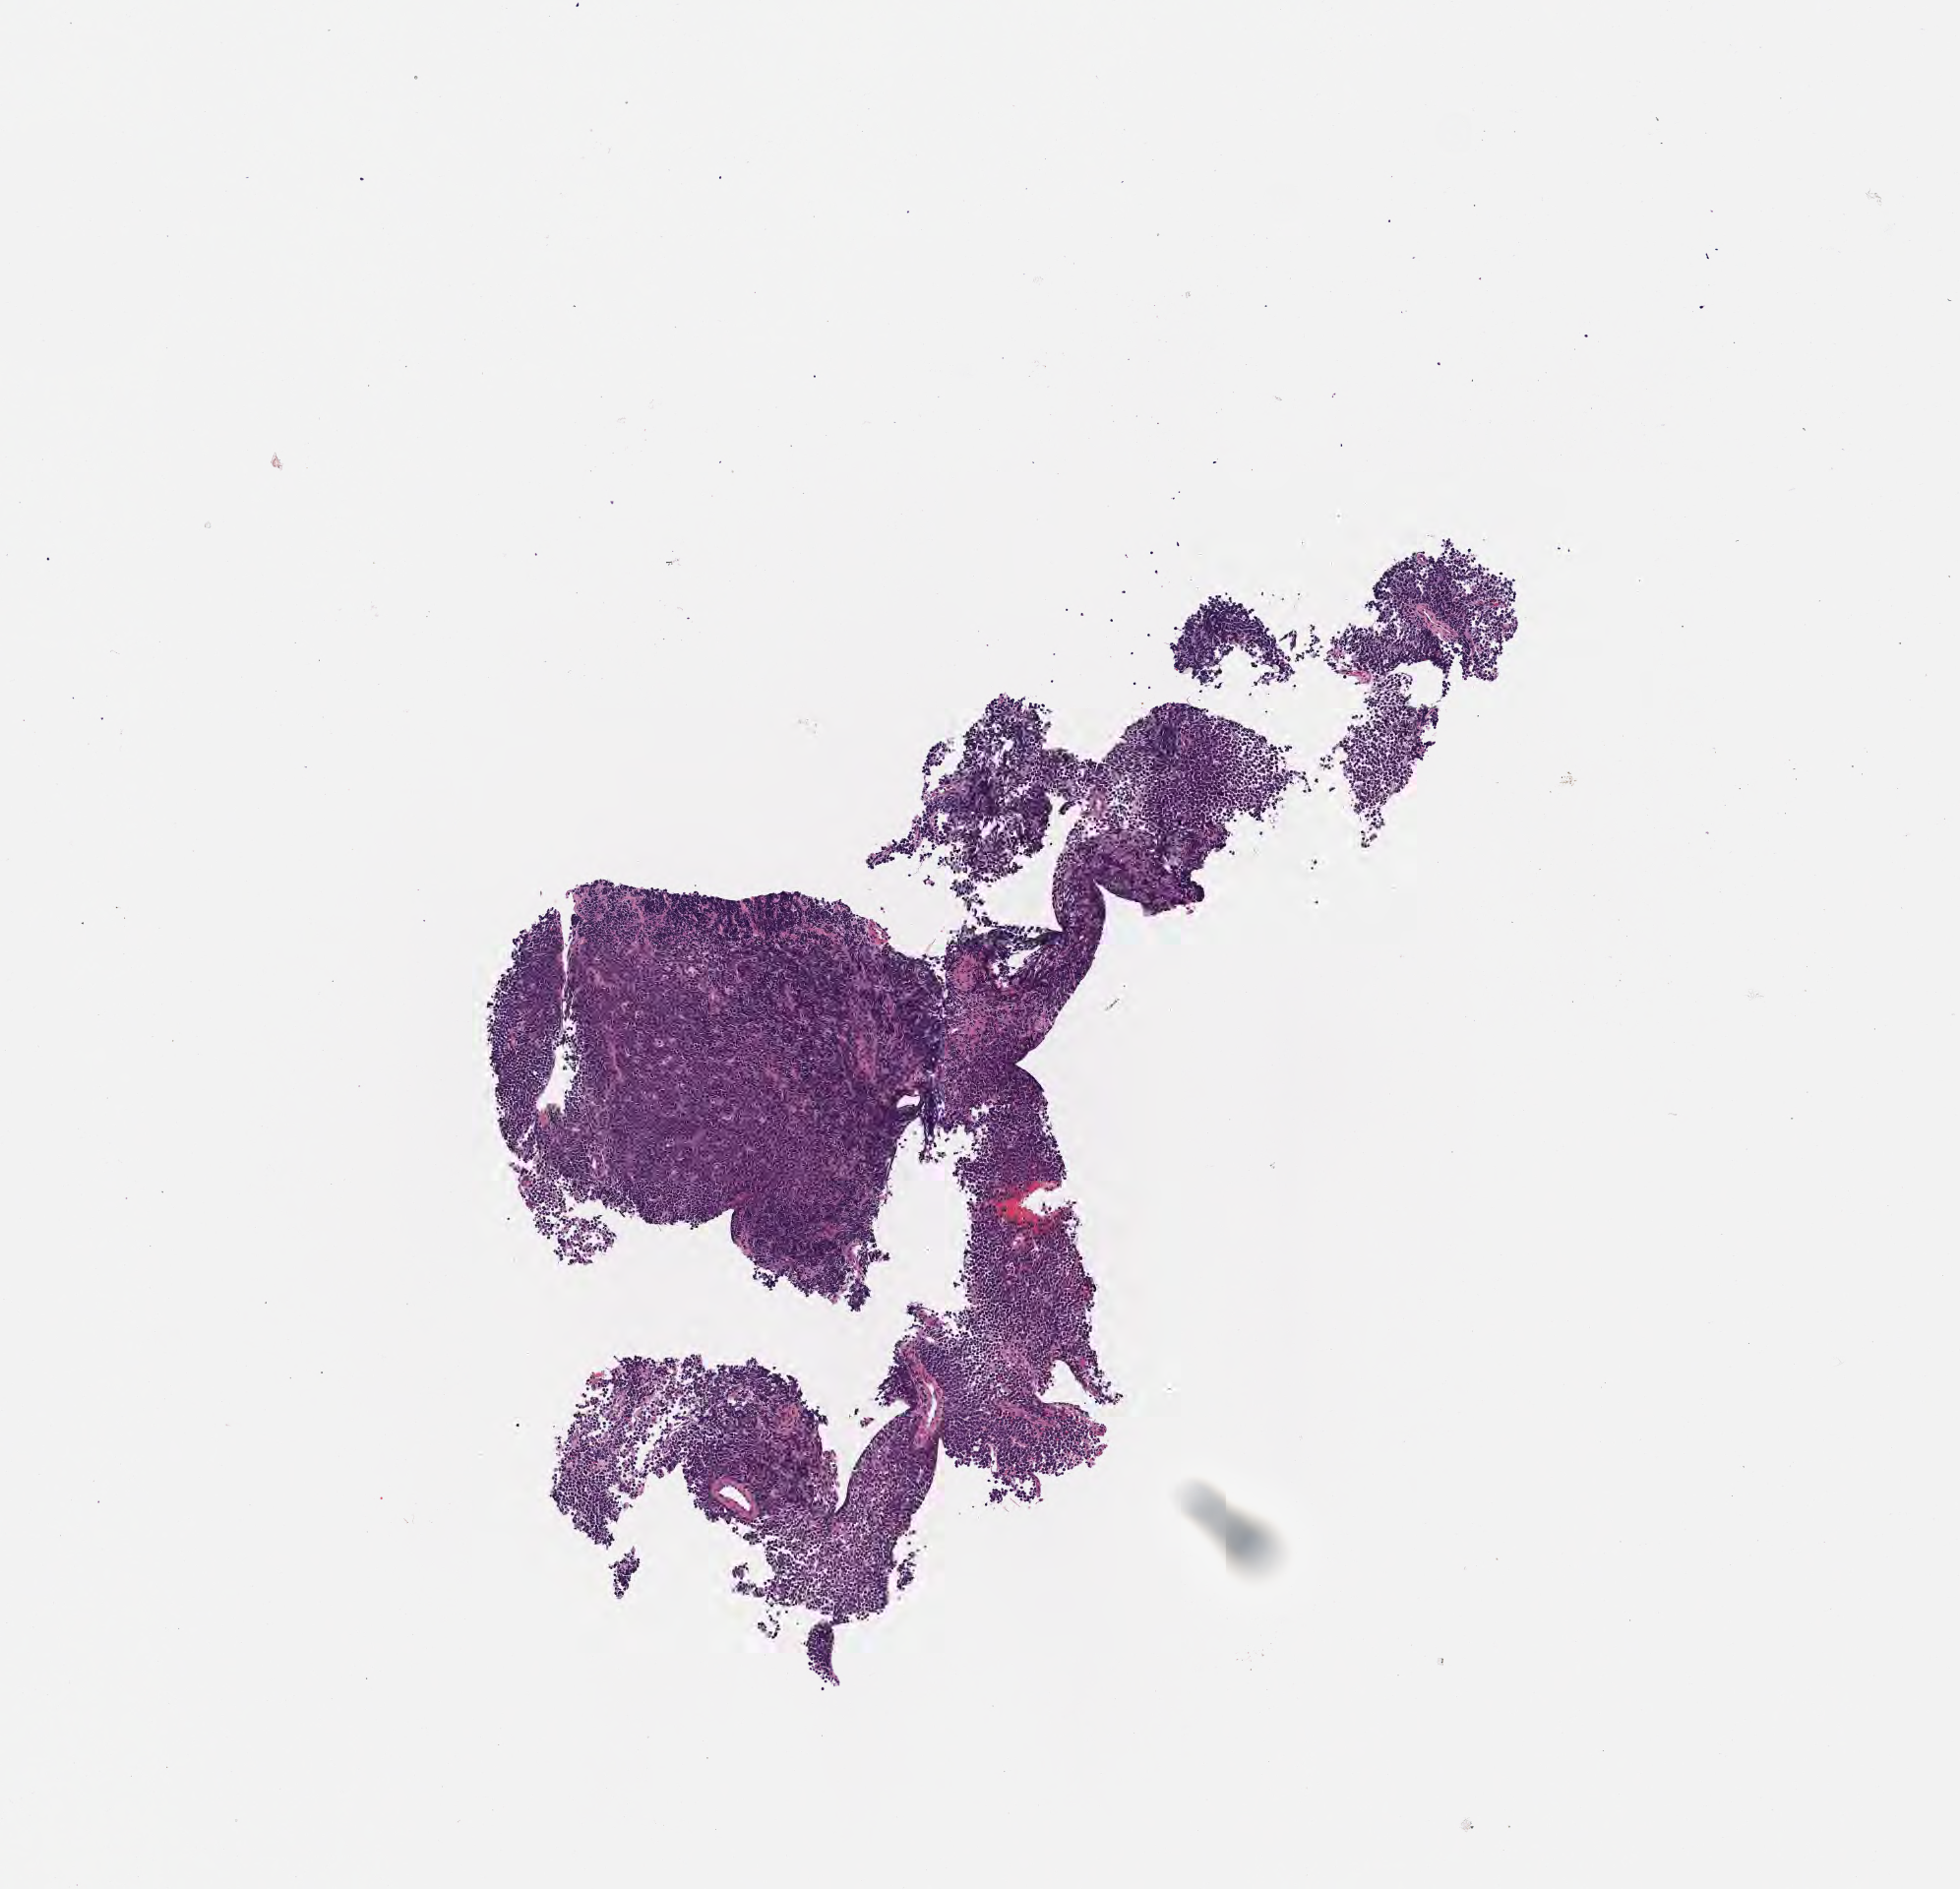
H&E whole-slide image, low-resolution overview of the scanned area, about 4.0 x 3.9 mm, tumor tissue. Male, age 8 years at initial diagnosis.
Histologic diagnosis: Burkitt lymphoma, NOS.